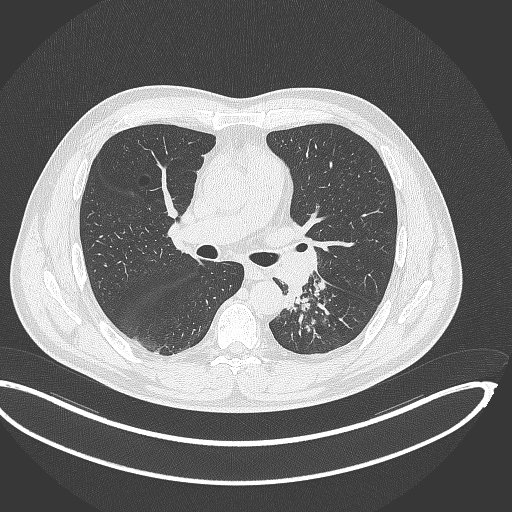
Chest CT, one axial slice. Position 208 of 362 along the scan axis. Reconstruction kernel B70f. Lung window (W 1500 / L -600 HU). 1 mm slice thickness. 512 × 512 image matrix, field of view 442 × 442 mm. Male patient, age 50 years. Case-level facts recorded for this patient, not image findings: clinical TNM (as recorded): T2a N3 M0.
Annotated regions visible in this slice (rectangle marked by the reading radiologist):
- lung tumour (recorded histology: squamous cell carcinoma): box from (x=280, y=282) to (x=306, y=311) px